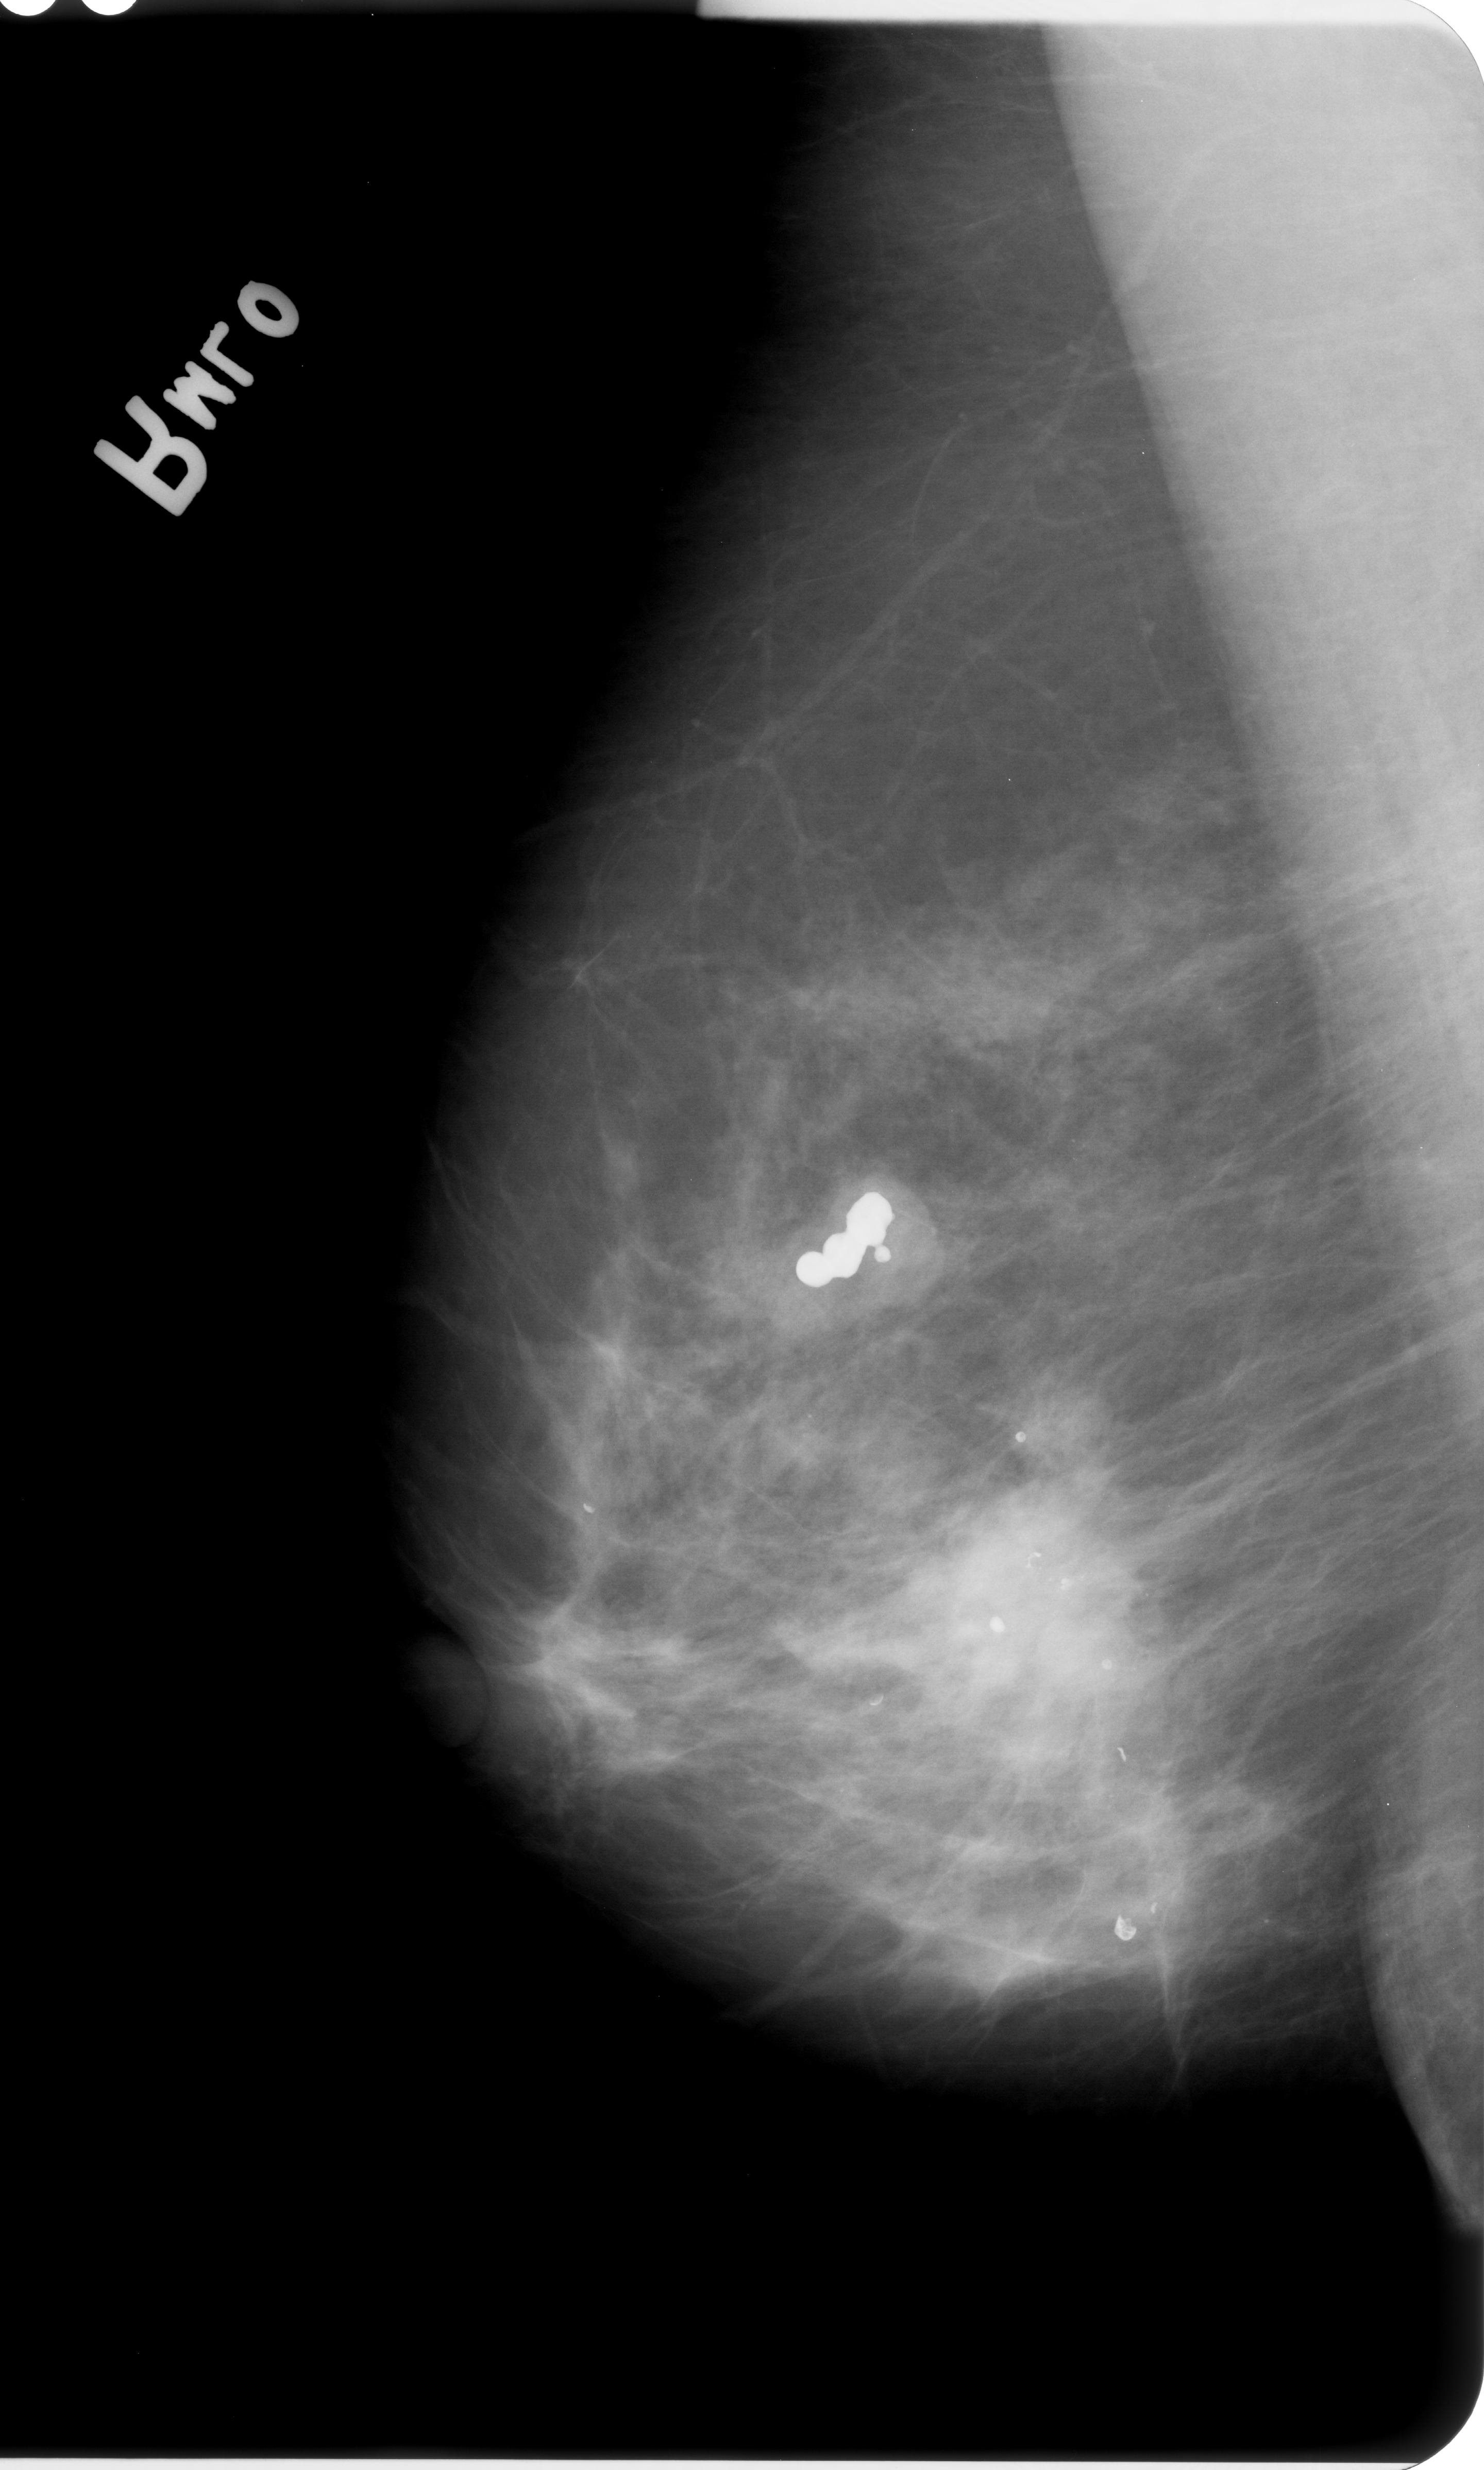
Digitized screen-film mammogram, right breast, MLO view, breast composition: heterogeneously dense (BI-RADS density category 3 of 4).
- Mass, shape architectural distortion, margins spiculated; BI-RADS assessment category 4; pathology (as recorded): malignant.